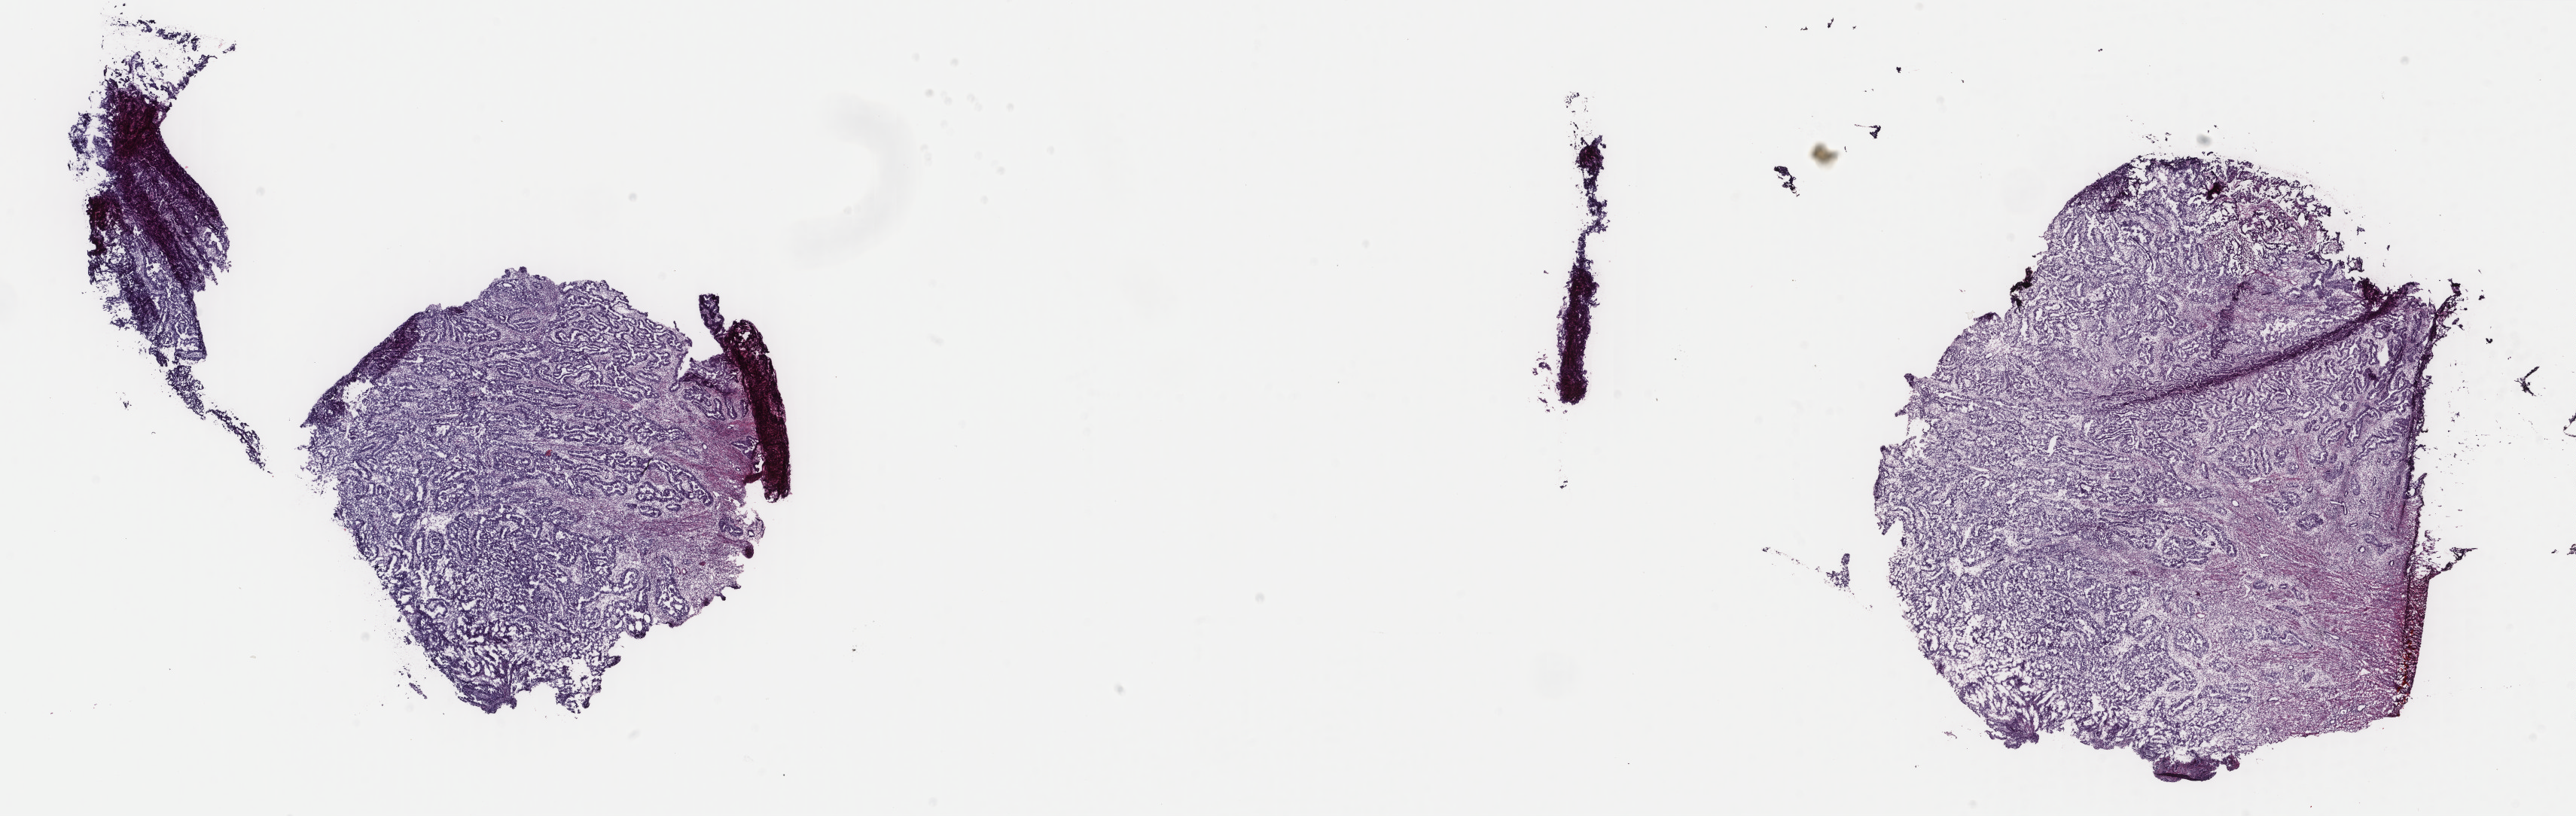
Whole-slide histology image, H&E, whole scanned area (about 27.2 x 8.6 mm) shown as a low-resolution overview. Frozen section. Primary tumour sample from the uterus. Female patient; age at initial diagnosis 59 years. Histologic grade: G3 (poorly differentiated). Pathologist review of this section (percent, as recorded): tumour cells 75%, tumour nuclei 75%, normal cells 2%, stromal cells 23%, necrosis 0%. Infiltration values recorded for this section: lymphocyte infiltration 8%, monocyte infiltration 0%, neutrophil infiltration 1%.
- FIGO stage: IVA
- lymph nodes positive (case pathology): 0 of 19 examined
- histologic diagnosis: Serous cystadenocarcinoma, NOS (endometrium)